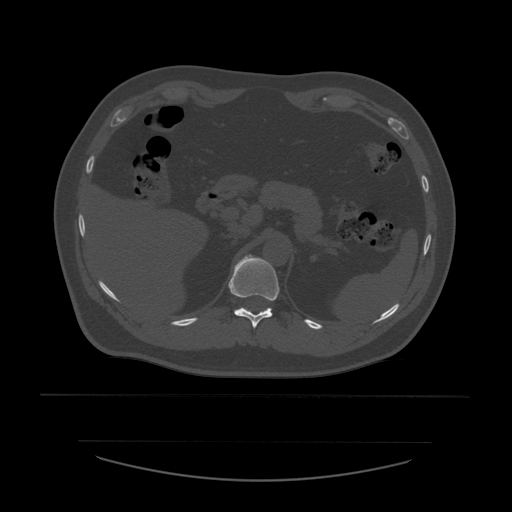
CT including the spine, one axial slice; position 272 of 532 along the scan axis; 120 kVp; bone window (W 1800 / L 400 HU); 1.25 mm slice thickness; 512 × 512 image matrix, field of view 441 × 441 mm. Patient age 44 years. Case-level facts recorded for this patient, not image findings: primary cancer: soft tissue sarcoma.
Outlined on this slice (semi-automatic segmentation, software-assisted and operator-edited):
- T11 vertebra: box from (x=229, y=255) to (x=280, y=329) px